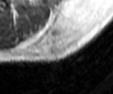
MRI of an extremity soft-tissue mass, one axial slice. Slice 33 of 42 in the series (ordered by position). MR volume resampled by the dataset authors to the PET/CT grid (not the native acquisition matrix). 113 × 94 image matrix. Male patient. From the clinical record (not read from this slice): histological type: leiomyosarcoma; grade: intermediate; site of the primary tumour: left pelvis.
Outlined on this slice (expert contour drawn on MRI and transferred to this co-registered scan by the dataset authors):
- gross tumour volume (mass): bounding box <38,20,75,60> (left, top, right, bottom; pixels)